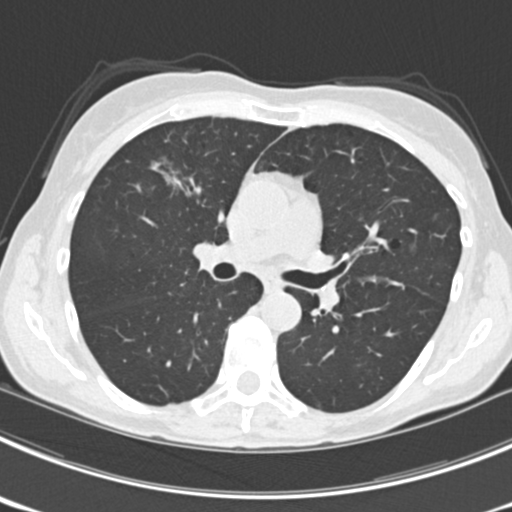
Chest CT (low-dose screening protocol), one axial image. Third annual screen. Lung window (W 1500 / L -600 HU). 2 mm slice thickness. Female participant, aged 63 years at enrolment. Current smoker at enrolment.
Expert-annotated lung lesion, box from (x=147, y=149) to (x=208, y=205) px. The screening reader recorded 9 non-calcified nodules or masses ≥4 mm on this exam (left upper lobe, right upper lobe, left upper lobe, left lower lobe, right middle lobe, left lower lobe, left lower lobe, right lower lobe, right lower lobe); which of them this box marks is not recorded. Official screen result: positive, other. Lung cancer was diagnosed 15 days after this screen: bronchiolo-alveolar adenocarcinoma, NOS, right upper lobe, right middle lobe, right lower lobe, left upper lobe, left lower lobe, moderately differentiated (G2), stage IV (AJCC 6th edition).